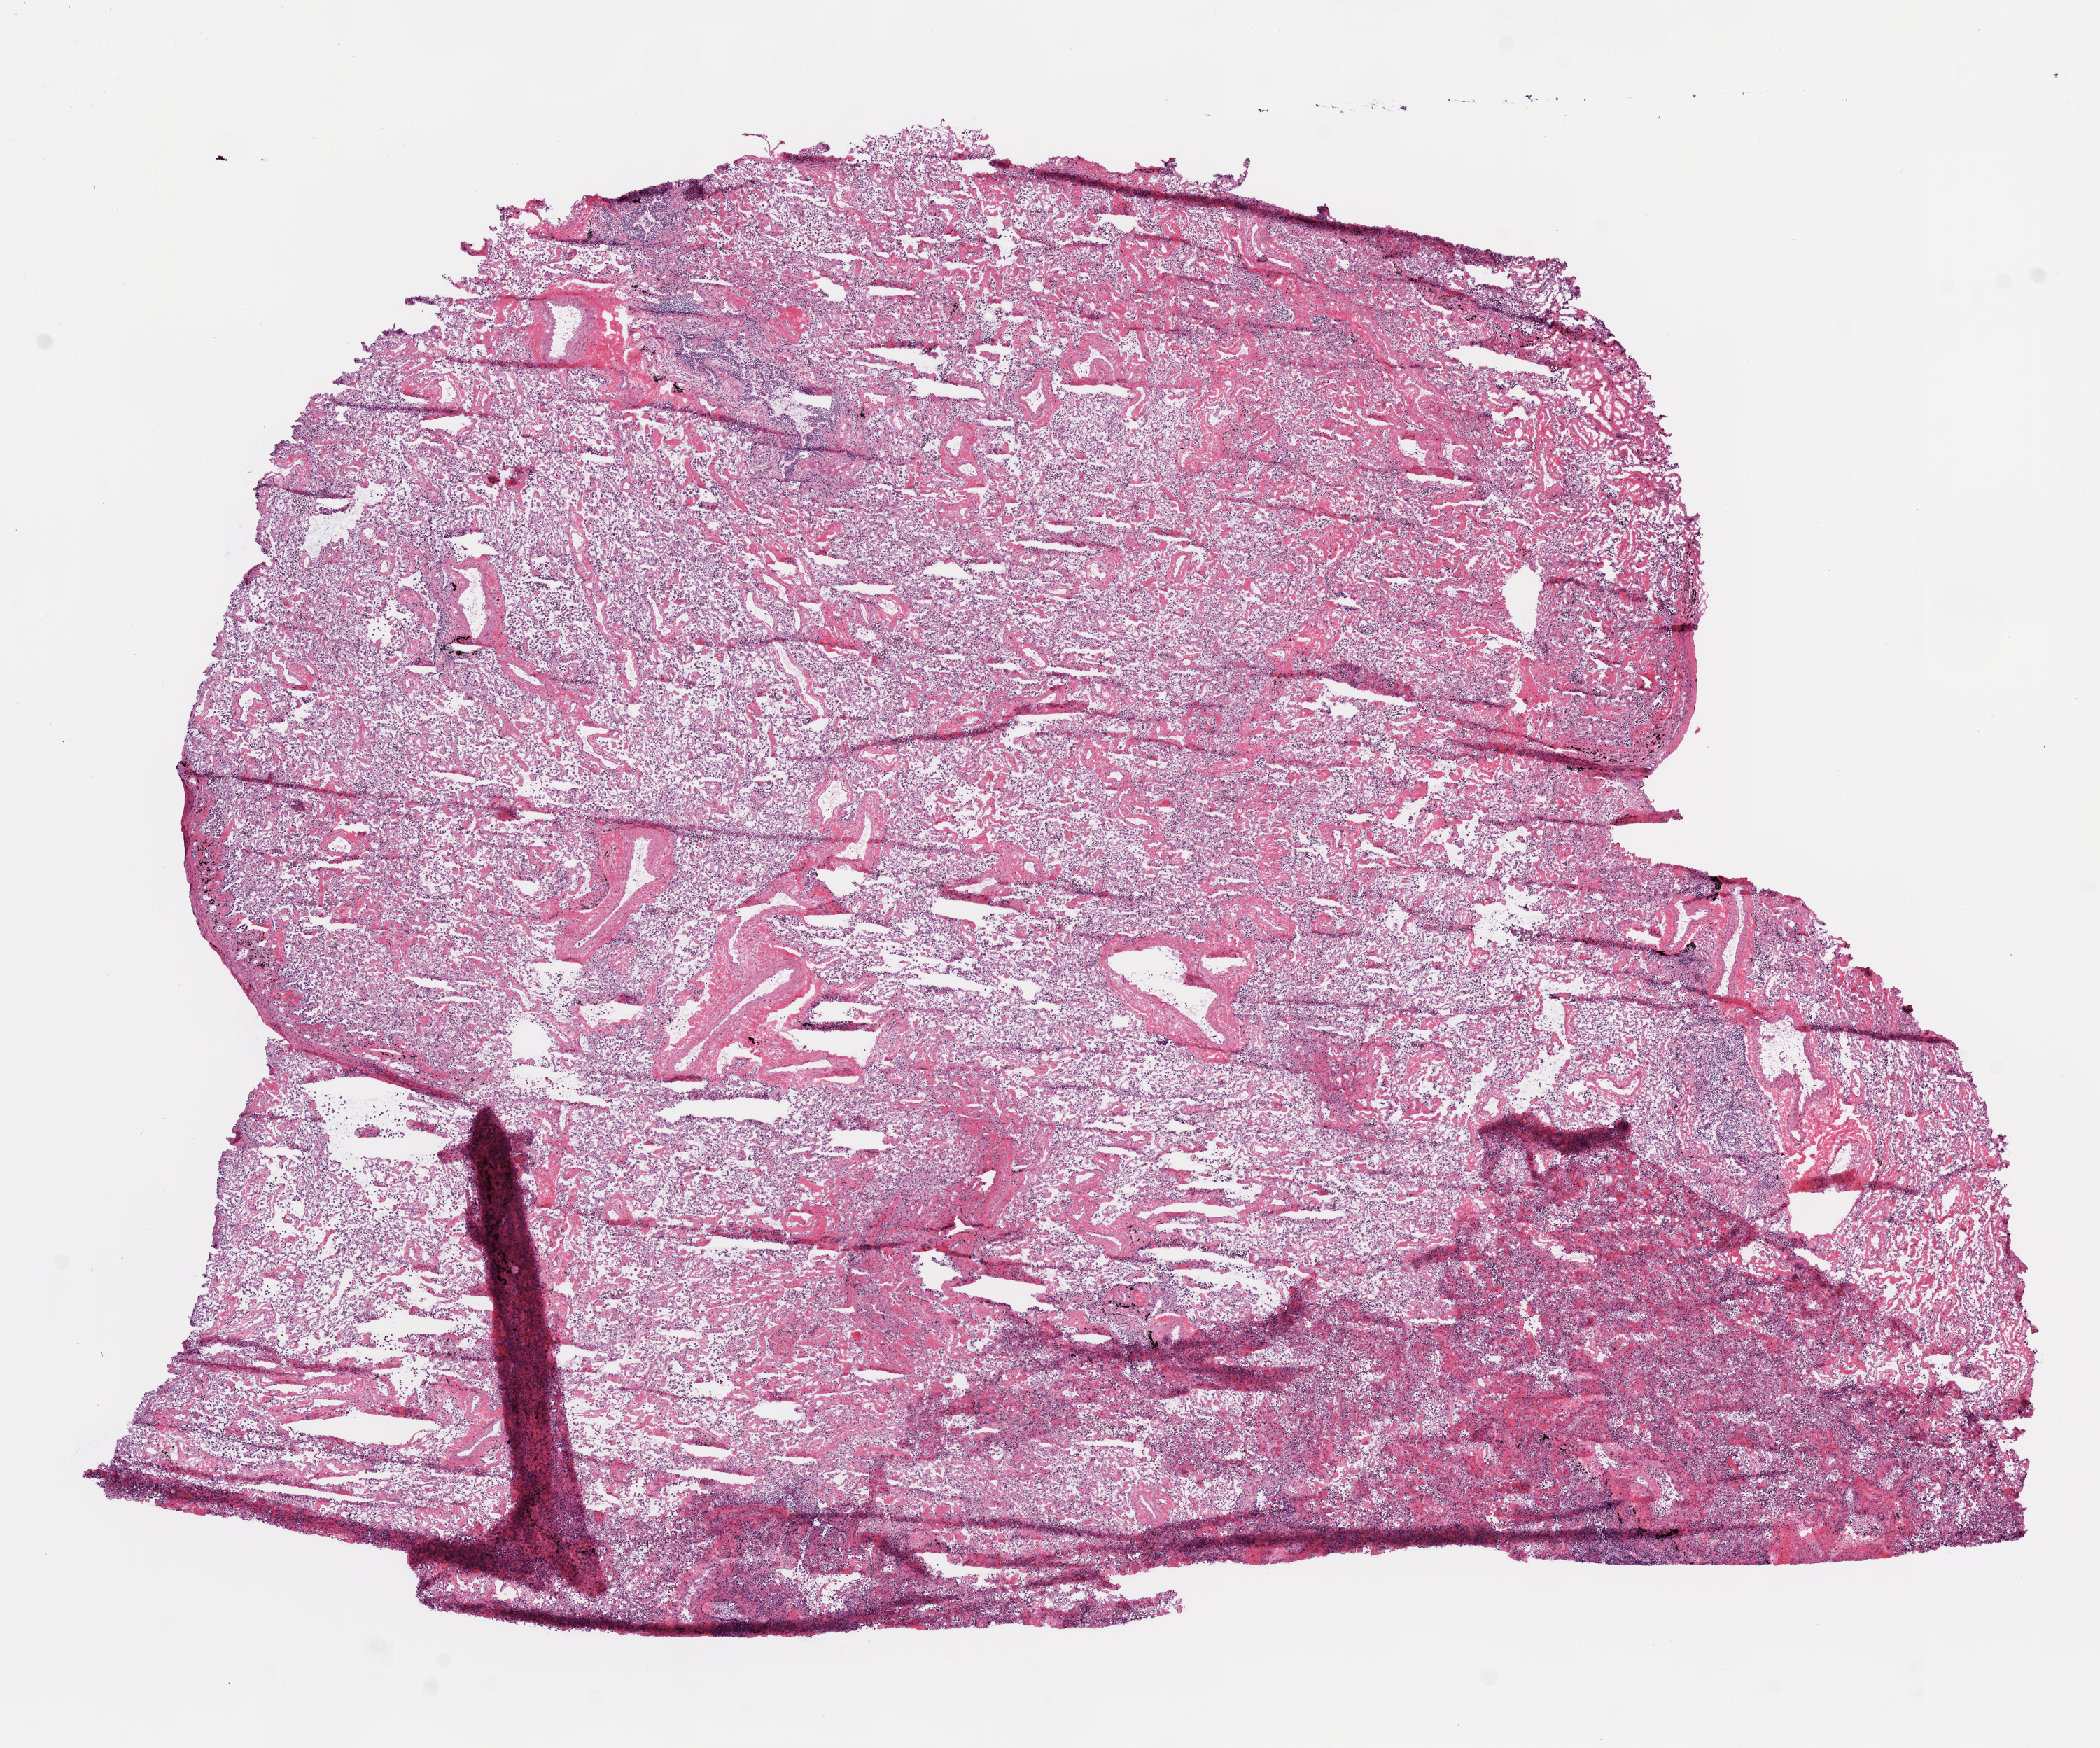
Digitized Hematoxylin and eosin (H&E) stained tissue section (whole slide) — a low-resolution overview of the entire scanned area, about 12.0 x 10.0 mm. Frozen section from the bottom of the tissue portion. Solid tissue normal (non-tumour tissue) sample from the lung. Male, age 47 years at initial diagnosis.
This section: solid tissue normal (non-tumour) sample from the same patient. Patient diagnosis: Squamous cell carcinoma, NOS.